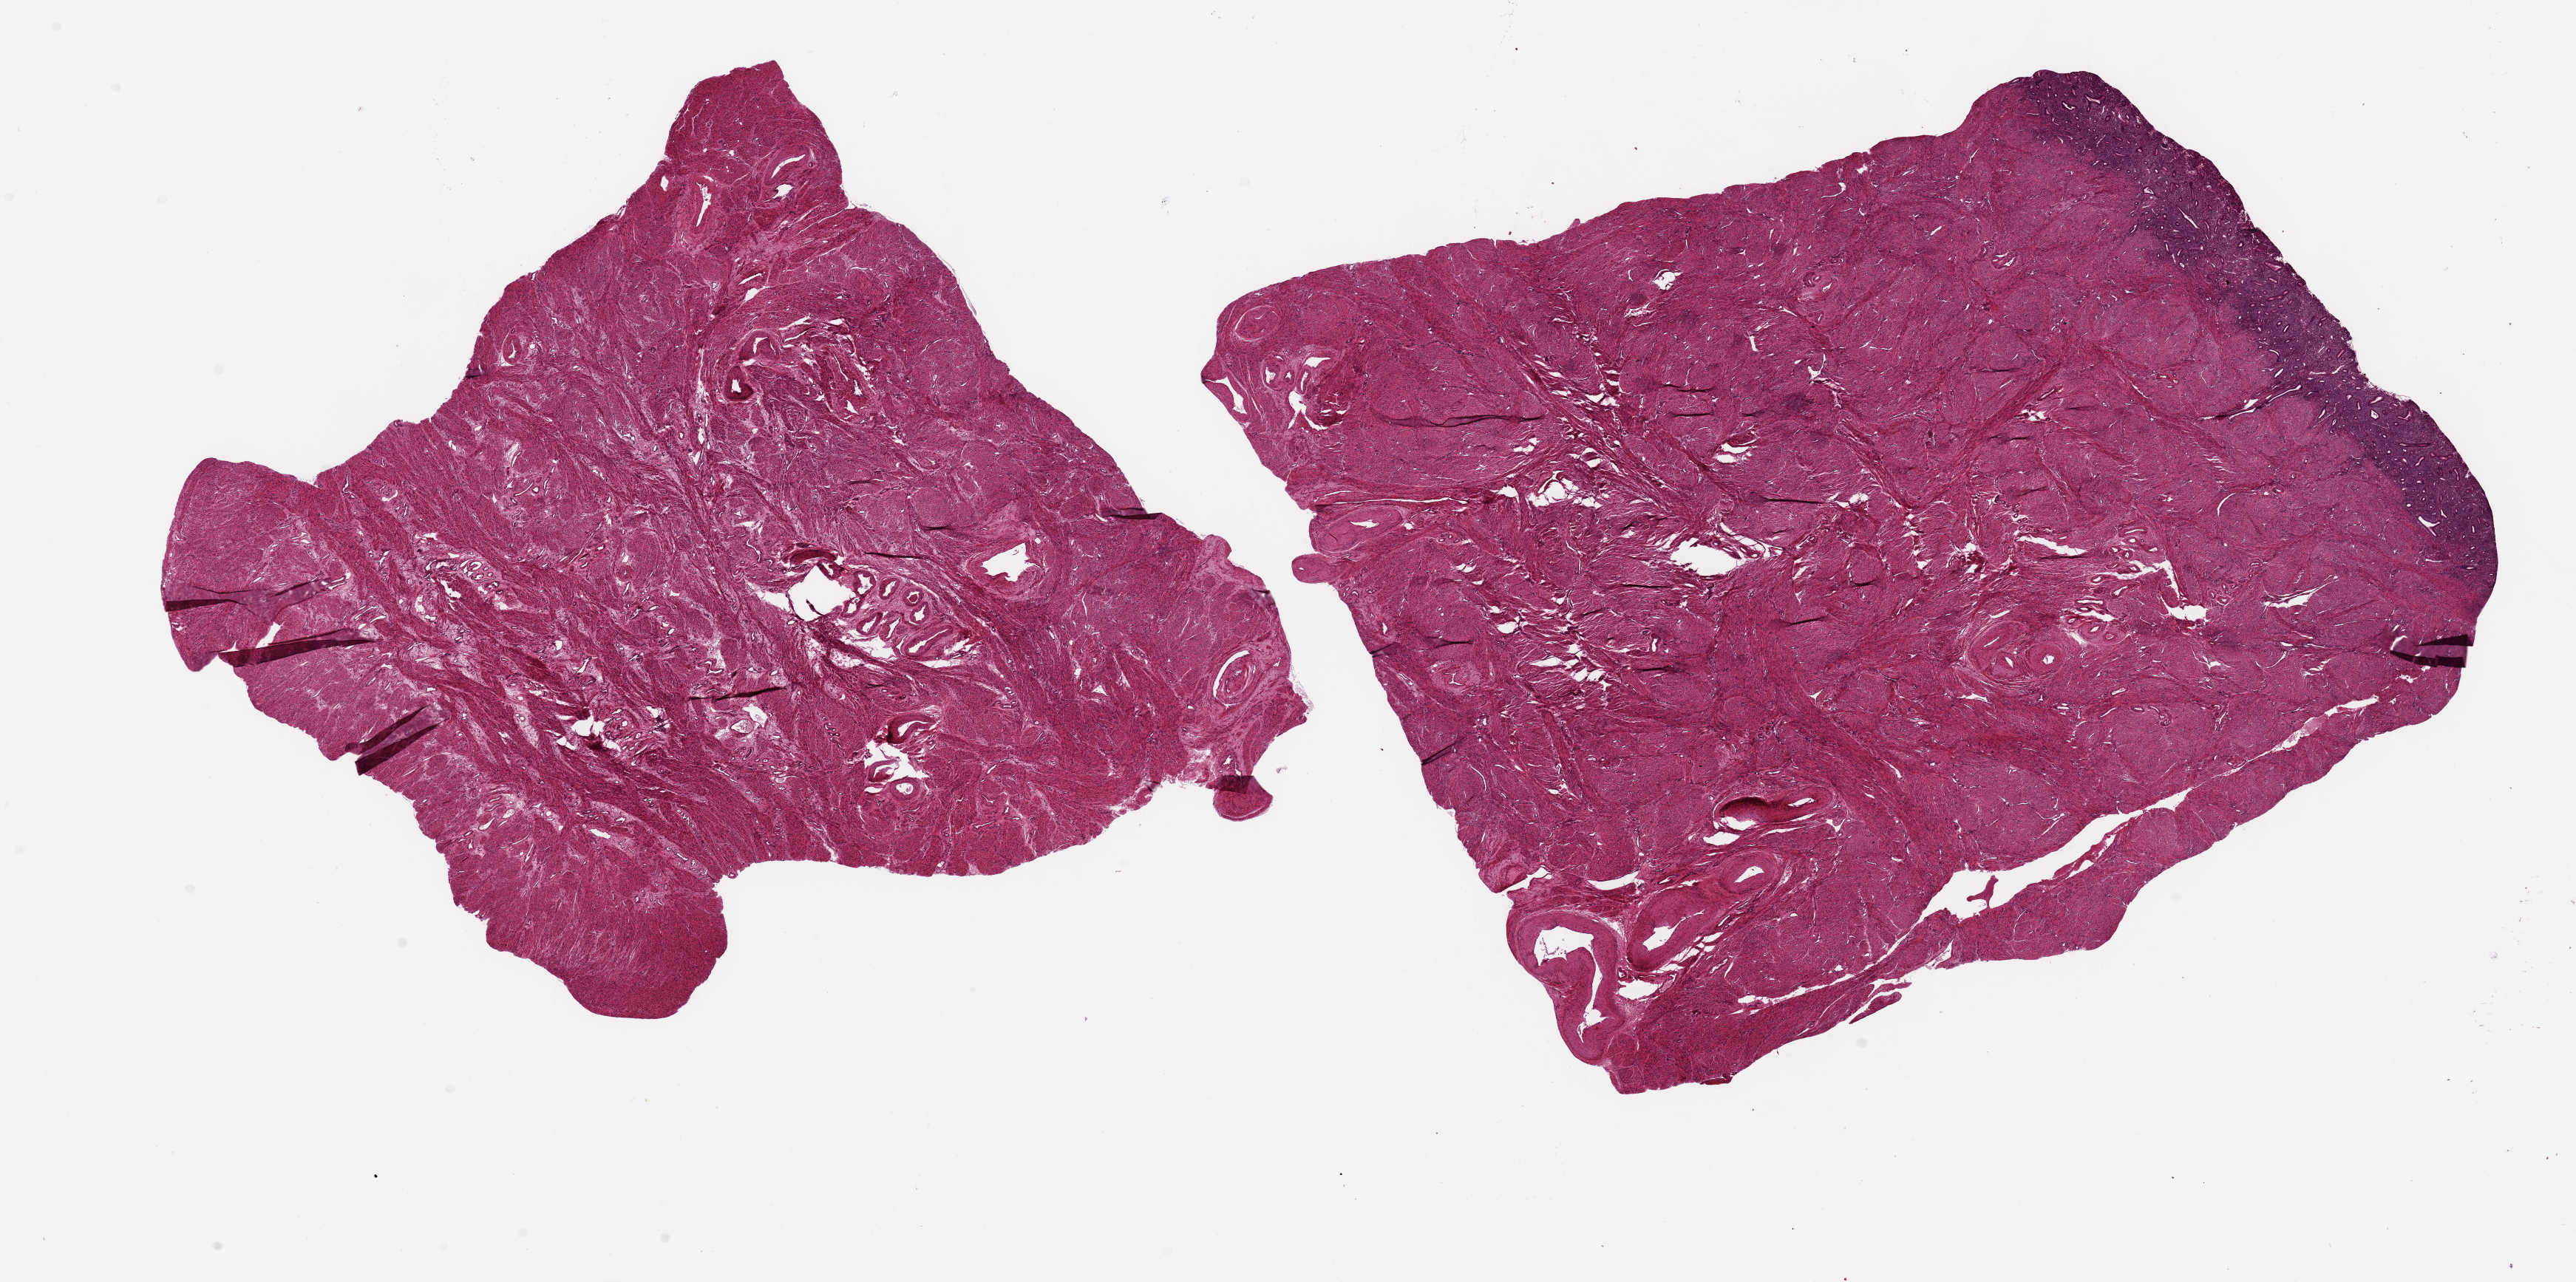
Whole-slide image, H&E stain — low-resolution overview of the scanned area, about 27.6 x 13.7 mm (slide scanned at 20x), PAXgene-fixed paraffin-embedded (PFPE) section, target tissue: uterus, donor tissue sample. Donor sex: female.
- pathologist's review note for this sample: 2 pieces 11x9 & 9x8 mm; endometrium (0.9 mm thick) on larger one; none on the other